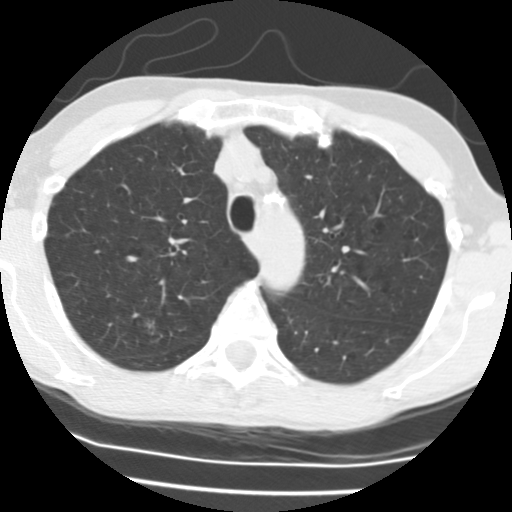
Low-dose screening chest CT, axial slice; third annual screen; lung window (W 1500 / L -600 HU); 2.5 mm slice thickness; standard (soft-tissue) reconstruction kernel (STANDARD); slice 163 of 195 in the series. Female, age 58 years at enrolment. Current smoker at enrolment.
Lesion marked by an expert reader, bounding box (x1, y1, x2, y2) in pixels: (131, 312, 169, 350). The screening reader recorded 3 non-calcified nodules or masses ≥4 mm on this exam (right upper lobe, left upper lobe, right upper lobe); which of them this box marks is not recorded. Official screen result: positive, other.